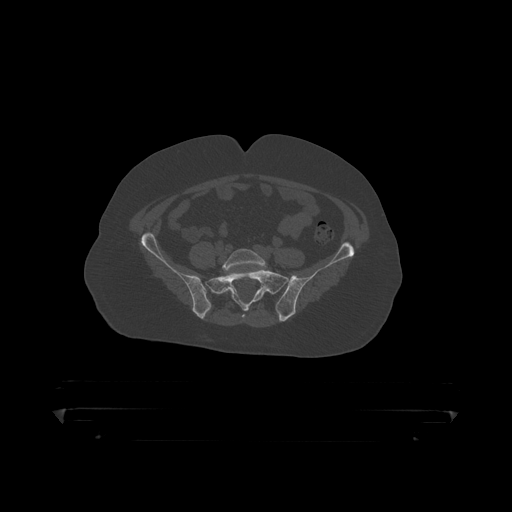
CT including the spine, one axial slice. Position 25 of 390 along the scan axis. 120 kVp. Bone window (W 1800 / L 400 HU). 512 × 512 image matrix. Male patient, age 60 years. From the clinical record (not read from this slice): primary cancer: prostate.
Structures marked on this image (semi-automatically segmented with operator editing):
- L5 vertebra: box from (x=223, y=249) to (x=267, y=295) px